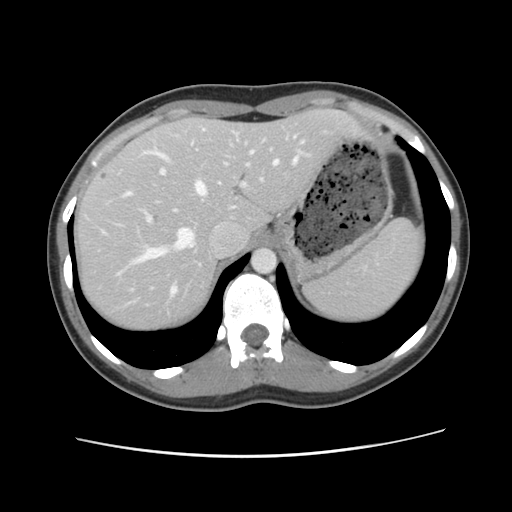
Contrast-enhanced abdominal CT, one axial slice; position 88 of 134 along the scan axis; intravenous contrast given; soft-tissue window (W 400 / L 40 HU); 2.5 mm slice thickness; 512 × 512 image matrix, field of view 339 × 339 mm. Female patient, age 33 years. From the clinical record (not read from this slice): diagnosis: colorectal cancer liver metastases, imaged before liver resection; multiple liver metastases: yes; largest metastasis: 4.5 cm; disease in both lobes: yes.
Structures marked on this image (outlined manually by an expert reader):
- hepatic veins: bounding box [x1, y1, x2, y2] px = [103, 129, 303, 295]
- liver: [74, 110, 363, 332]
- planned liver remnant (the part of the liver to remain after resection): [75, 110, 362, 332]
- portal vein (with intrahepatic branches): [139, 139, 288, 224]
- liver metastasis: [99, 171, 109, 181]